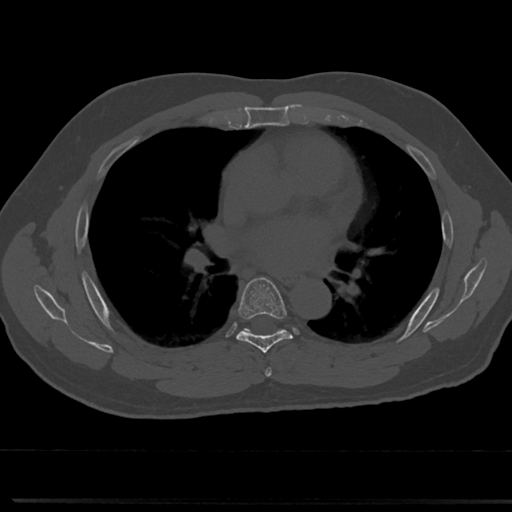
CT including the spine, one axial slice; slice 449 of 817 in the series (ordered by position); 120 kVp; bone window (W 1800 / L 400 HU); 512 × 512 image matrix. Patient: male, 61 years. From the clinical record (not read from this slice): primary cancer: prostate.
Annotated regions visible in this slice (semi-automatic segmentation, software-assisted and operator-edited):
- T5 vertebra: box from (x=264, y=349) to (x=273, y=376) px
- T6 vertebra: (x=218, y=277)–(x=311, y=354)